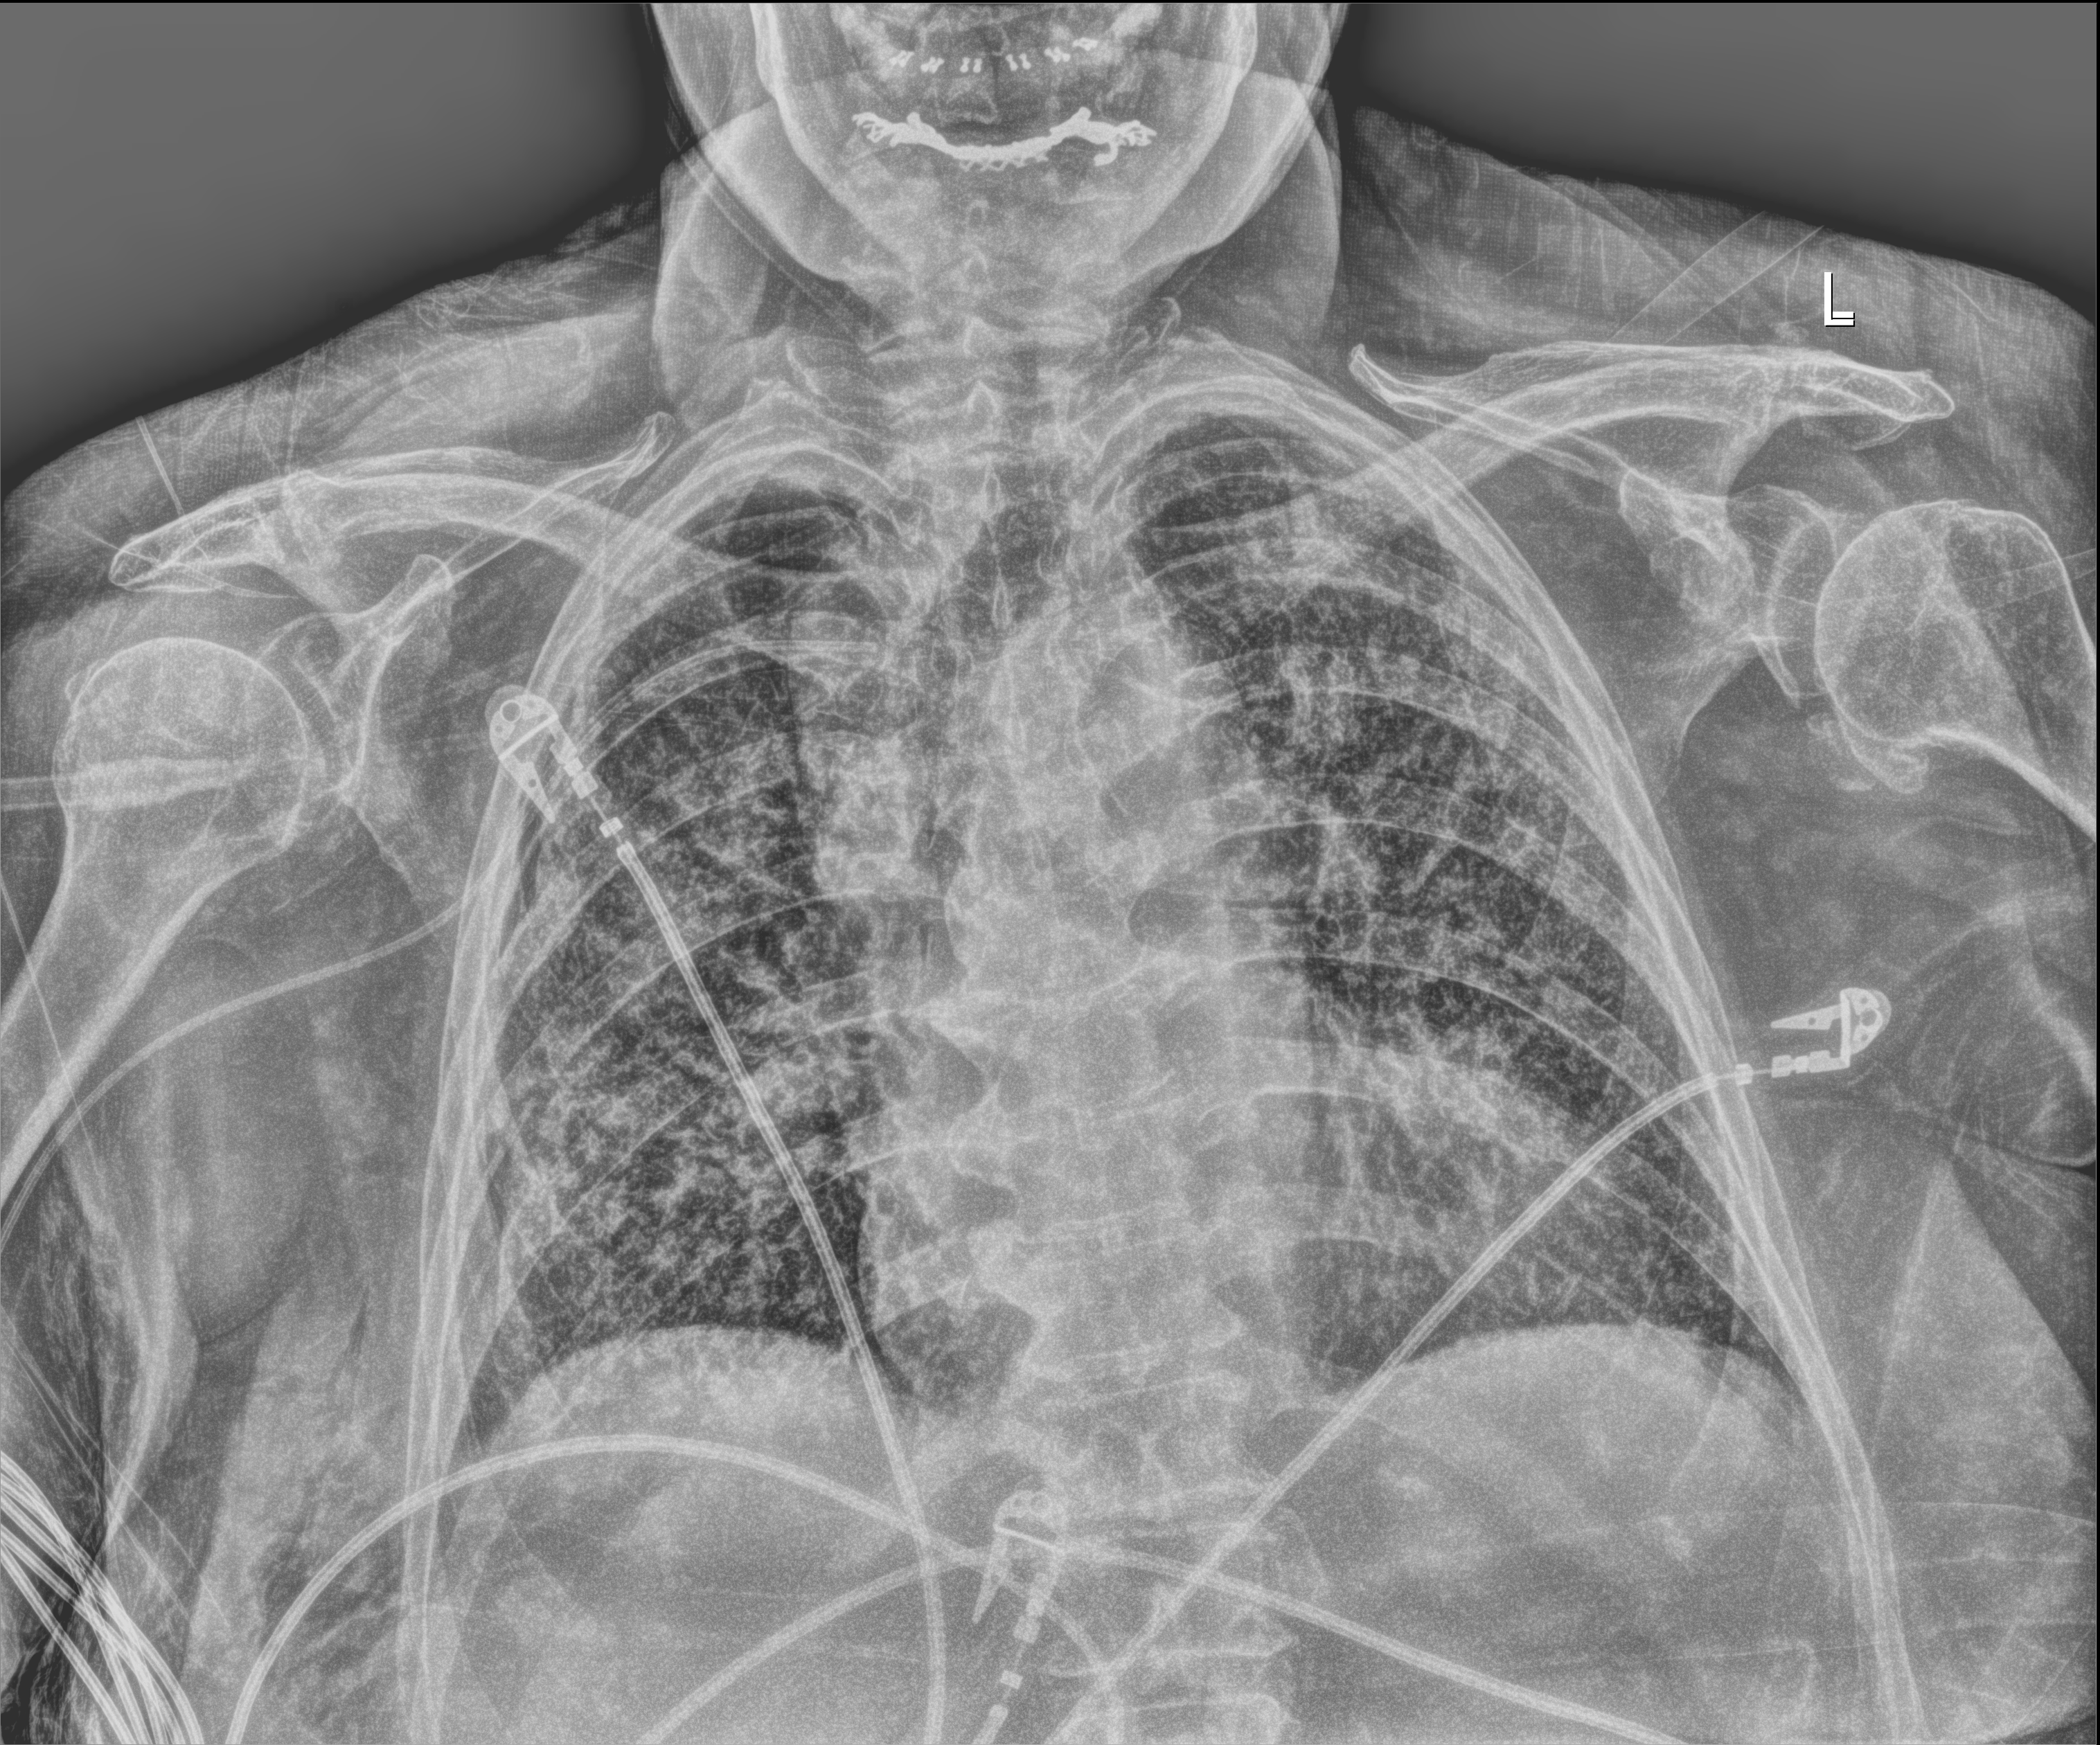
Chest X-ray (portable). Patient hospitalised with COVID-19; female, aged 75–90 years.
Hospital-stay facts (about this admission, not read from this image; timing relative to this image not recorded): admitted to intensive care during this hospital stay: no; mechanically ventilated during this hospital stay: yes.